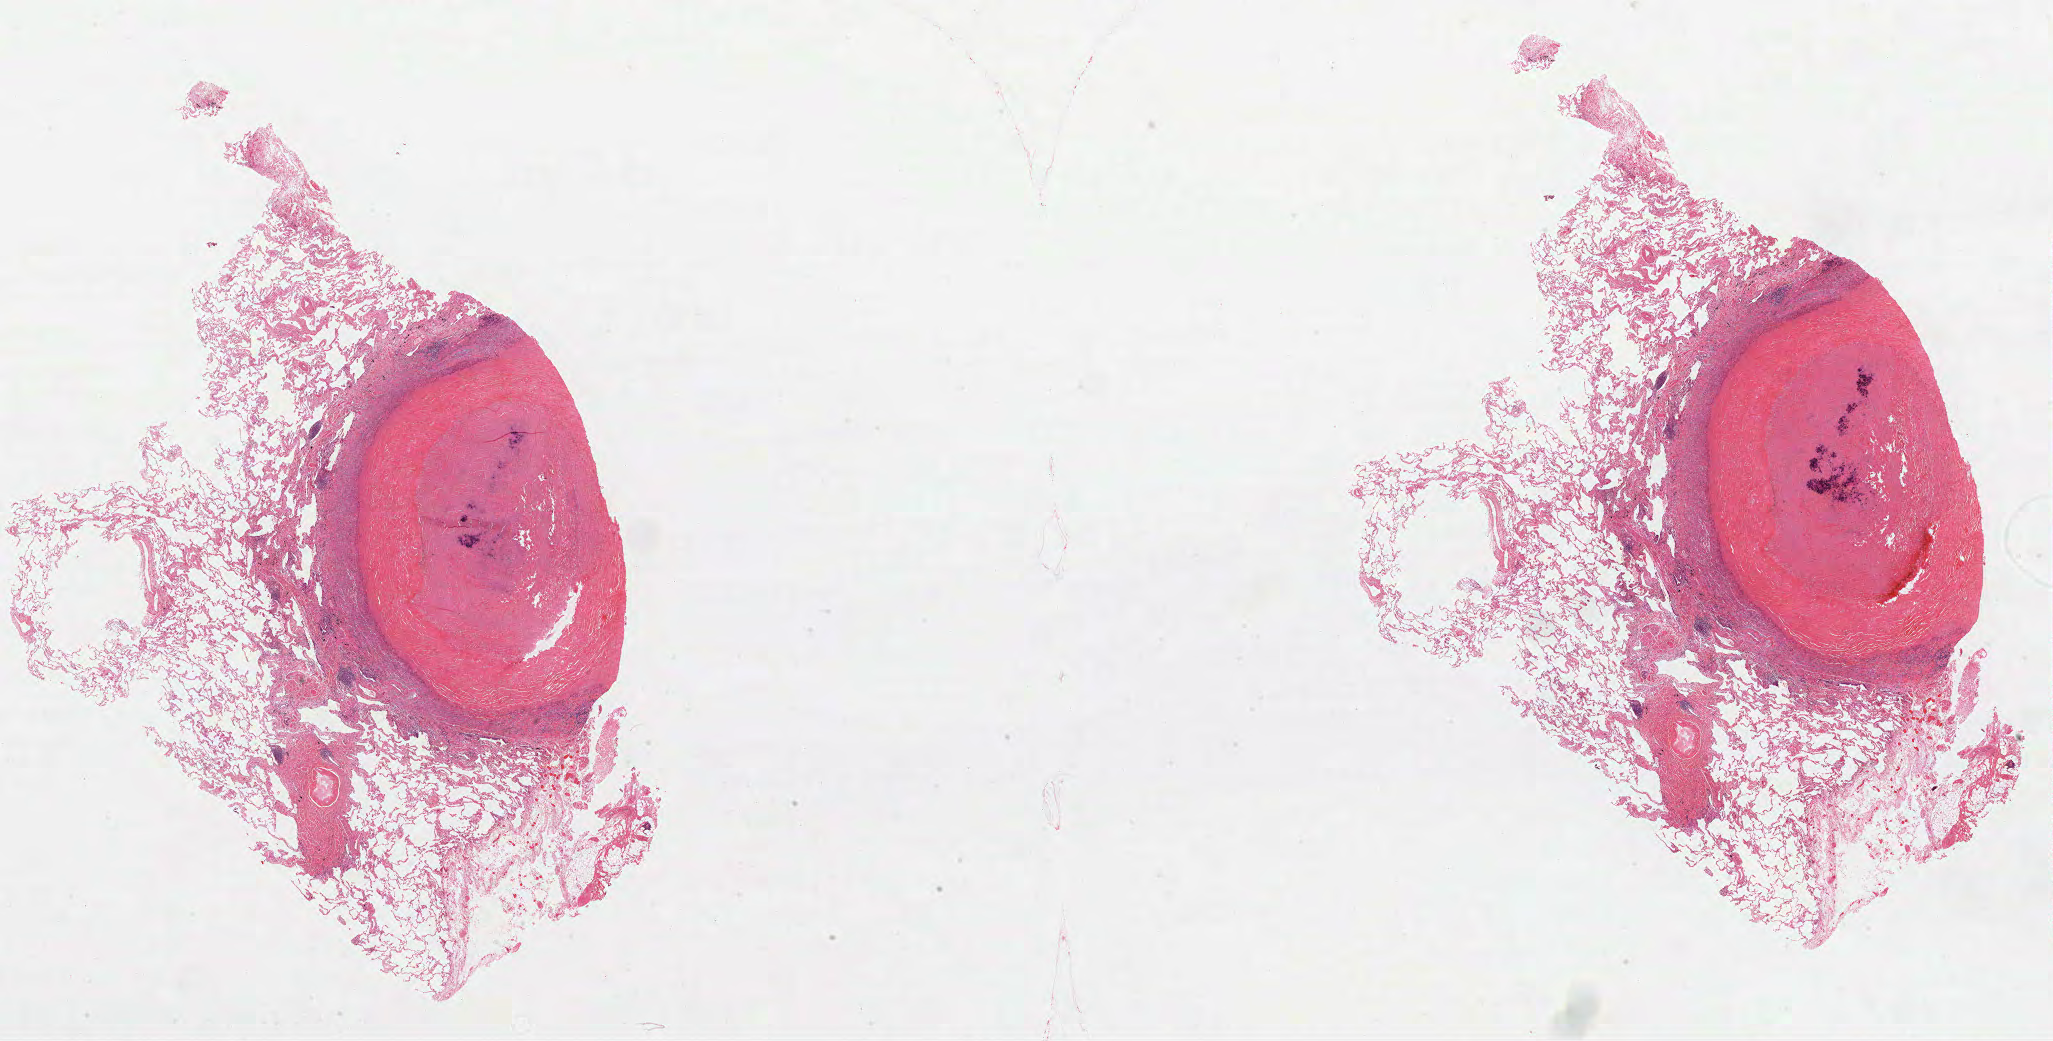
Whole-slide histology image, H&E-stained — low-resolution overview of the scanned area, about 33.1 x 16.8 mm (acquisition: 40x scan); FFPE section; primary tumour sample from the lung. Patient: female, age at initial diagnosis 75 years.
AJCC pathologic stage: IA (7th edition). Laterality: right. Diagnosis: Adenocarcinoma, NOS (upper lobe, lung).